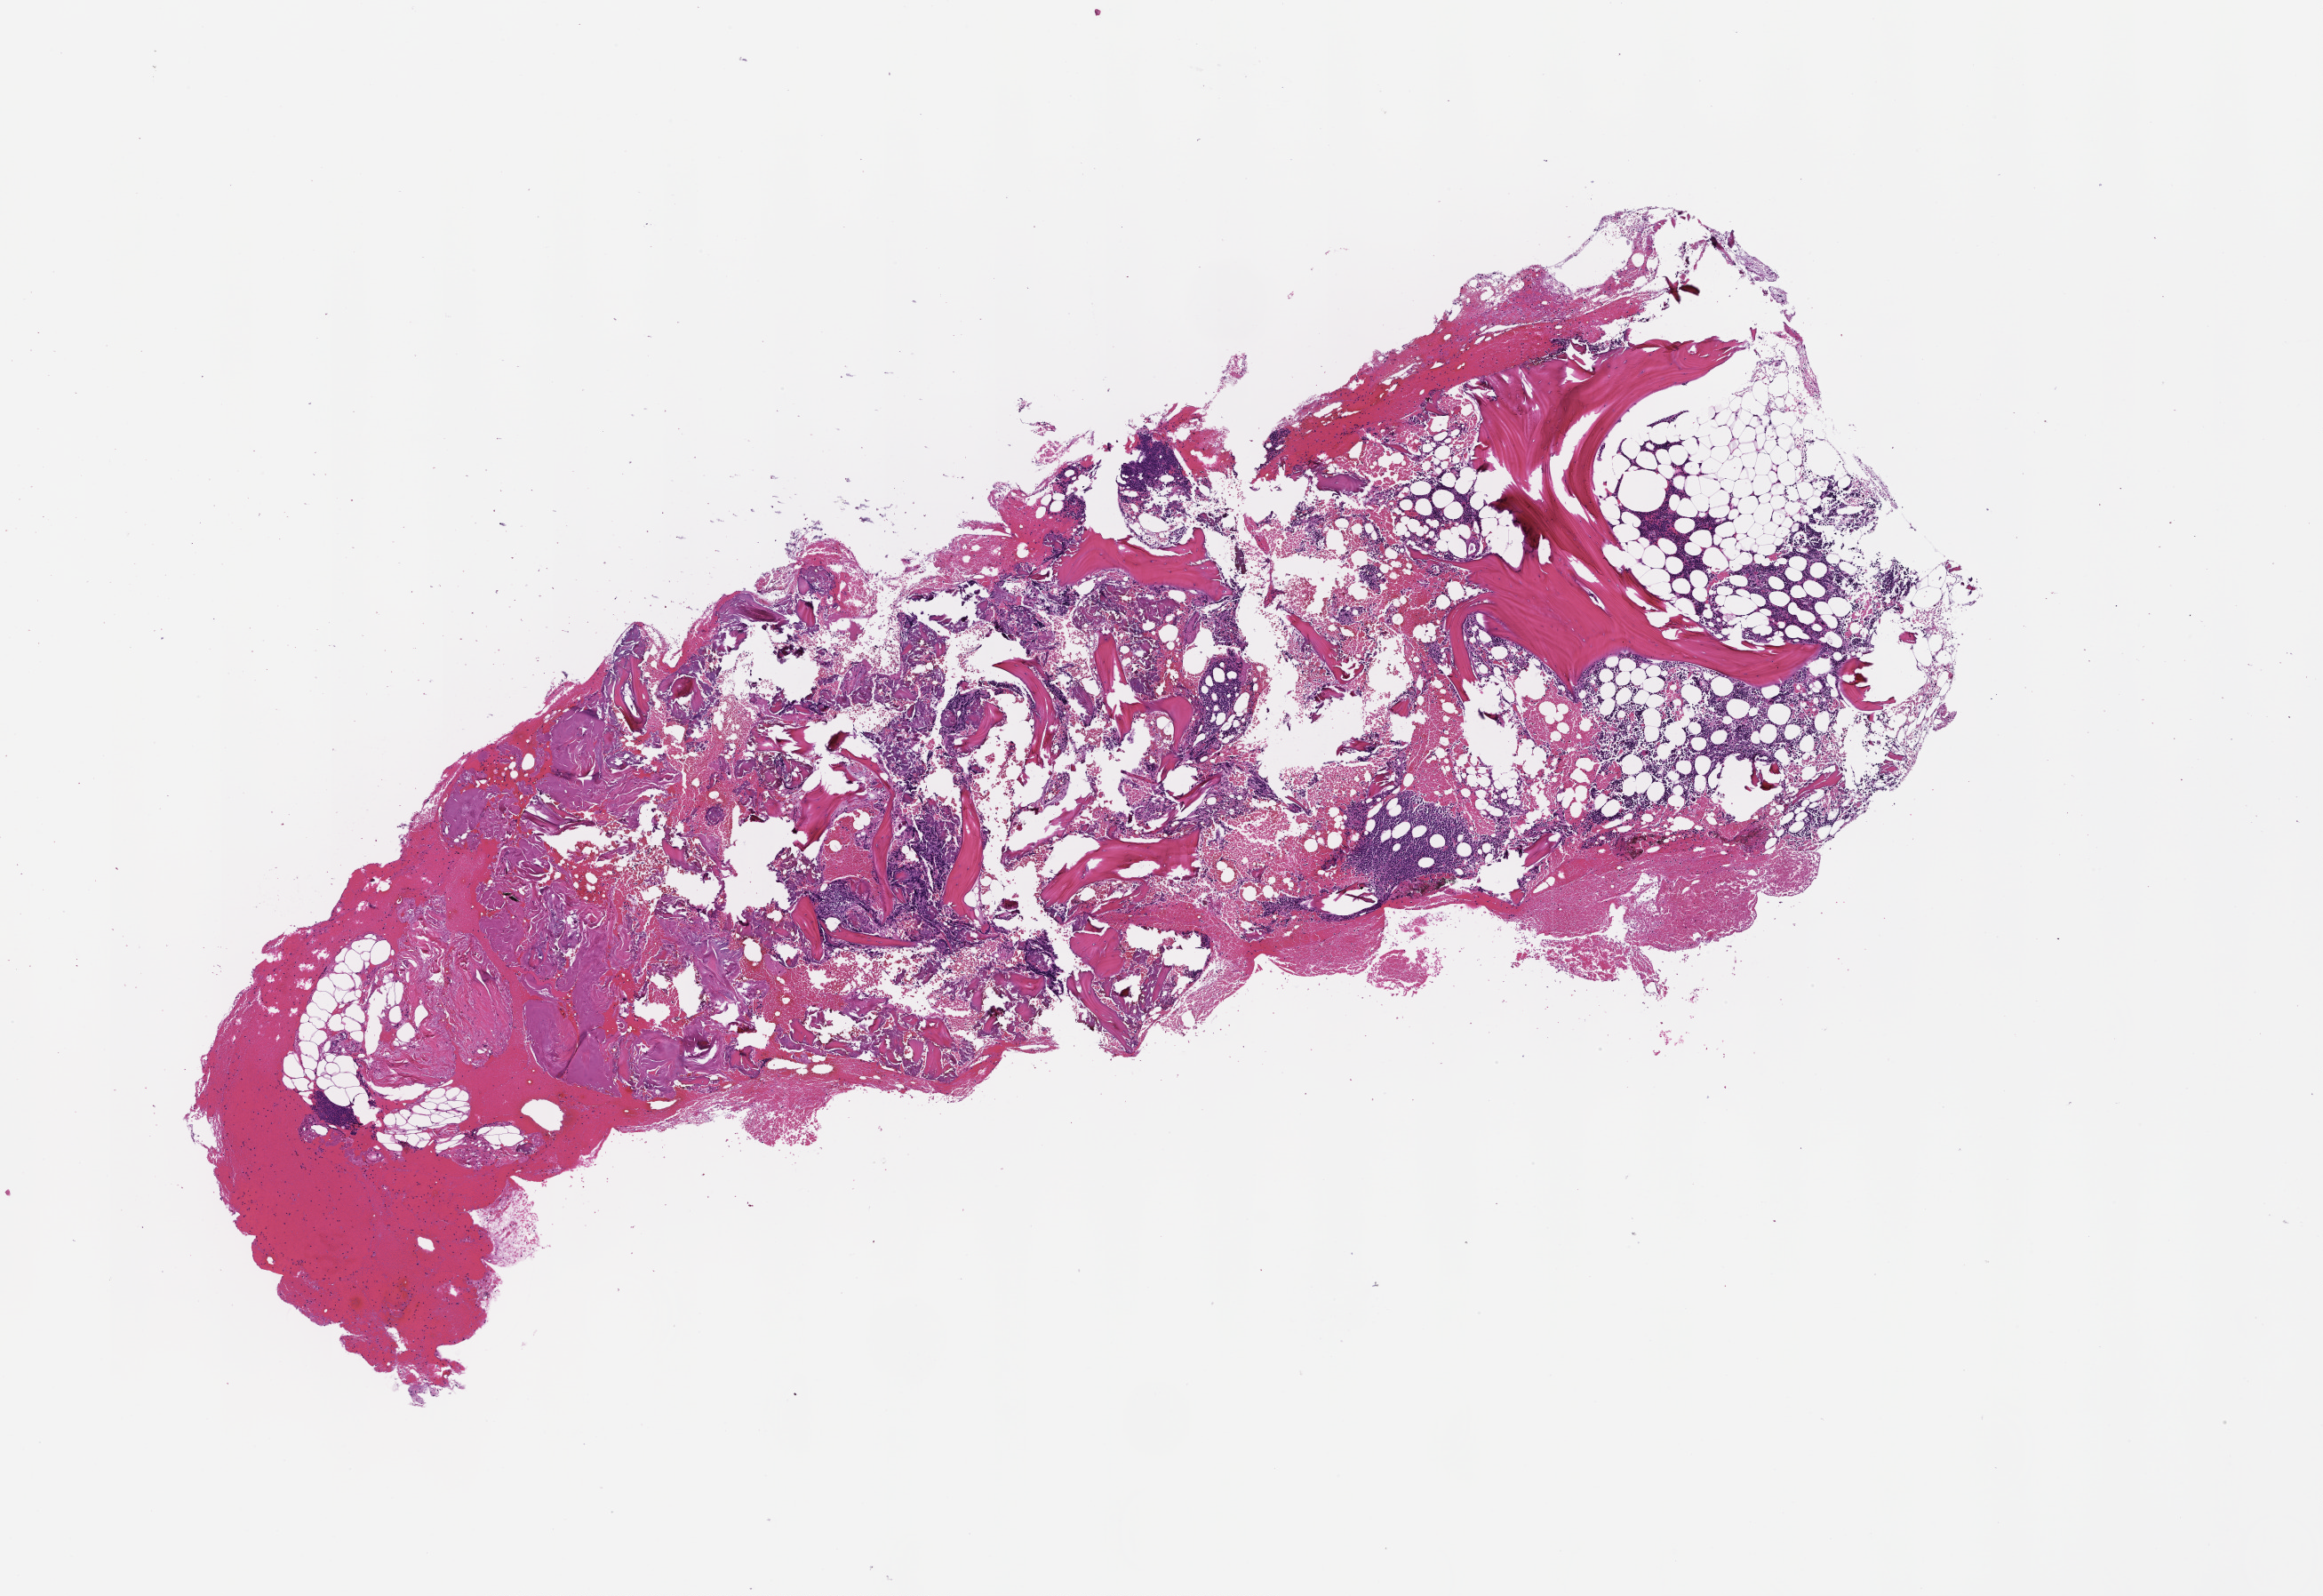
Digitized haematoxylin and eosin-stained section — whole scanned area (about 10.6 x 7.3 mm) shown as a low-resolution overview. Formalin-fixed, paraffin-embedded (FFPE) tissue. Tissue site: bone marrow. Collected at baseline (before treatment). Male patient.
This section: primary tumor. Diagnosis: Plasma Cell Myeloma.